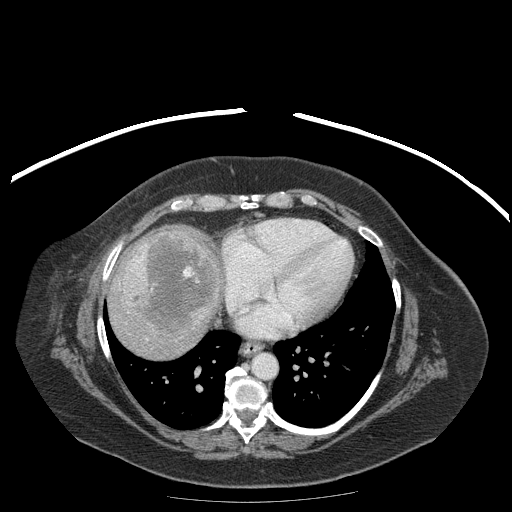
Contrast-enhanced abdominal CT (liver protocol), one axial slice; position 169 of 204 along the scan axis; reconstruction kernel STANDARD; soft-tissue window (W 400 / L 40 HU); 2.5 mm slice thickness; 512 × 512 image matrix, field of view 440 × 440 mm. From the clinical record (not read from this slice): diagnosis: hepatocellular carcinoma (patient treated with transarterial chemoembolisation; whether this scan precedes or follows treatment is not stated here); TNM stage (as recorded): Stage-IIIB; Child-Pugh class: A; tumour differentiation: well differentiated; tumour nodularity: uninodular.
Annotated regions visible in this slice (semi-automatic segmentation, software-assisted and operator-edited):
- liver parenchyma outside the tumour (the mass and vessels are separate outlines, so this box may not span the whole liver): bounding box <108,226,222,357> (left, top, right, bottom; pixels)
- mass: <119,232,221,336>